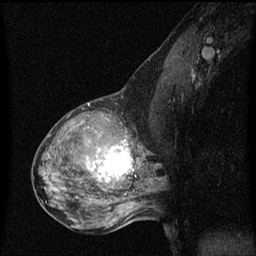
Breast MRI (dynamic contrast-enhanced), one sagittal slice; slice 34 of 60 in the series (ordered by position); dynamic contrast-enhanced series, image 2 of 3 at this slice position (ordered by acquisition); 1.5 T; TE 4.2 ms, TR 8 ms; 2 mm slice thickness; 256 × 256 image matrix. Female patient, age 50 years.
Structures marked on this image (semi-automatic segmentation, software-assisted and operator-edited):
- analysis volume of interest (the breast-tissue region the enhancement analysis was run in; not a lesion): bounding box (x1, y1, x2, y2) in pixels: (91, 126, 141, 189)
- tumour enhancement mask (voxels above the 70 % enhancement threshold inside the analysis volume of interest): (93, 142, 133, 181)